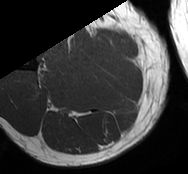
MRI of an extremity soft-tissue mass, one axial slice. Slice 18 of 93 in the series (ordered by position). MR volume resampled by the dataset authors to the PET/CT grid (not the native acquisition matrix). 3.27 mm slice thickness. 188 × 174 image matrix, field of view 184 × 170 mm. Male patient. From the clinical record (not read from this slice): histological type: undifferentiated - pleiomorphic; grade: high; site of the primary tumour: right thigh.
Structures marked on this image (expert contour drawn on MRI and transferred to this co-registered scan by the dataset authors):
- gross tumour volume including surrounding oedema: box from (x=54, y=42) to (x=78, y=66) px